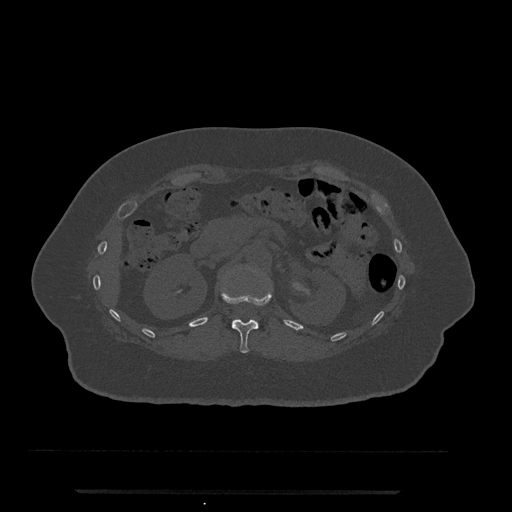
CT including the spine, one axial slice. Position 149 of 797 along the scan axis. Reconstruction kernel Br40s/3. Bone window (W 1800 / L 400 HU). 512 × 512 image matrix, field of view 440 × 440 mm. Patient: female, 51 years. From the clinical record (not read from this slice): primary cancer: neuro; vertebrae with lytic lesions (as recorded): T8.
Annotated regions visible in this slice (semi-automatically segmented with operator editing):
- T12 vertebra: bounding box (x1, y1, x2, y2) in pixels: (221, 288, 272, 353)